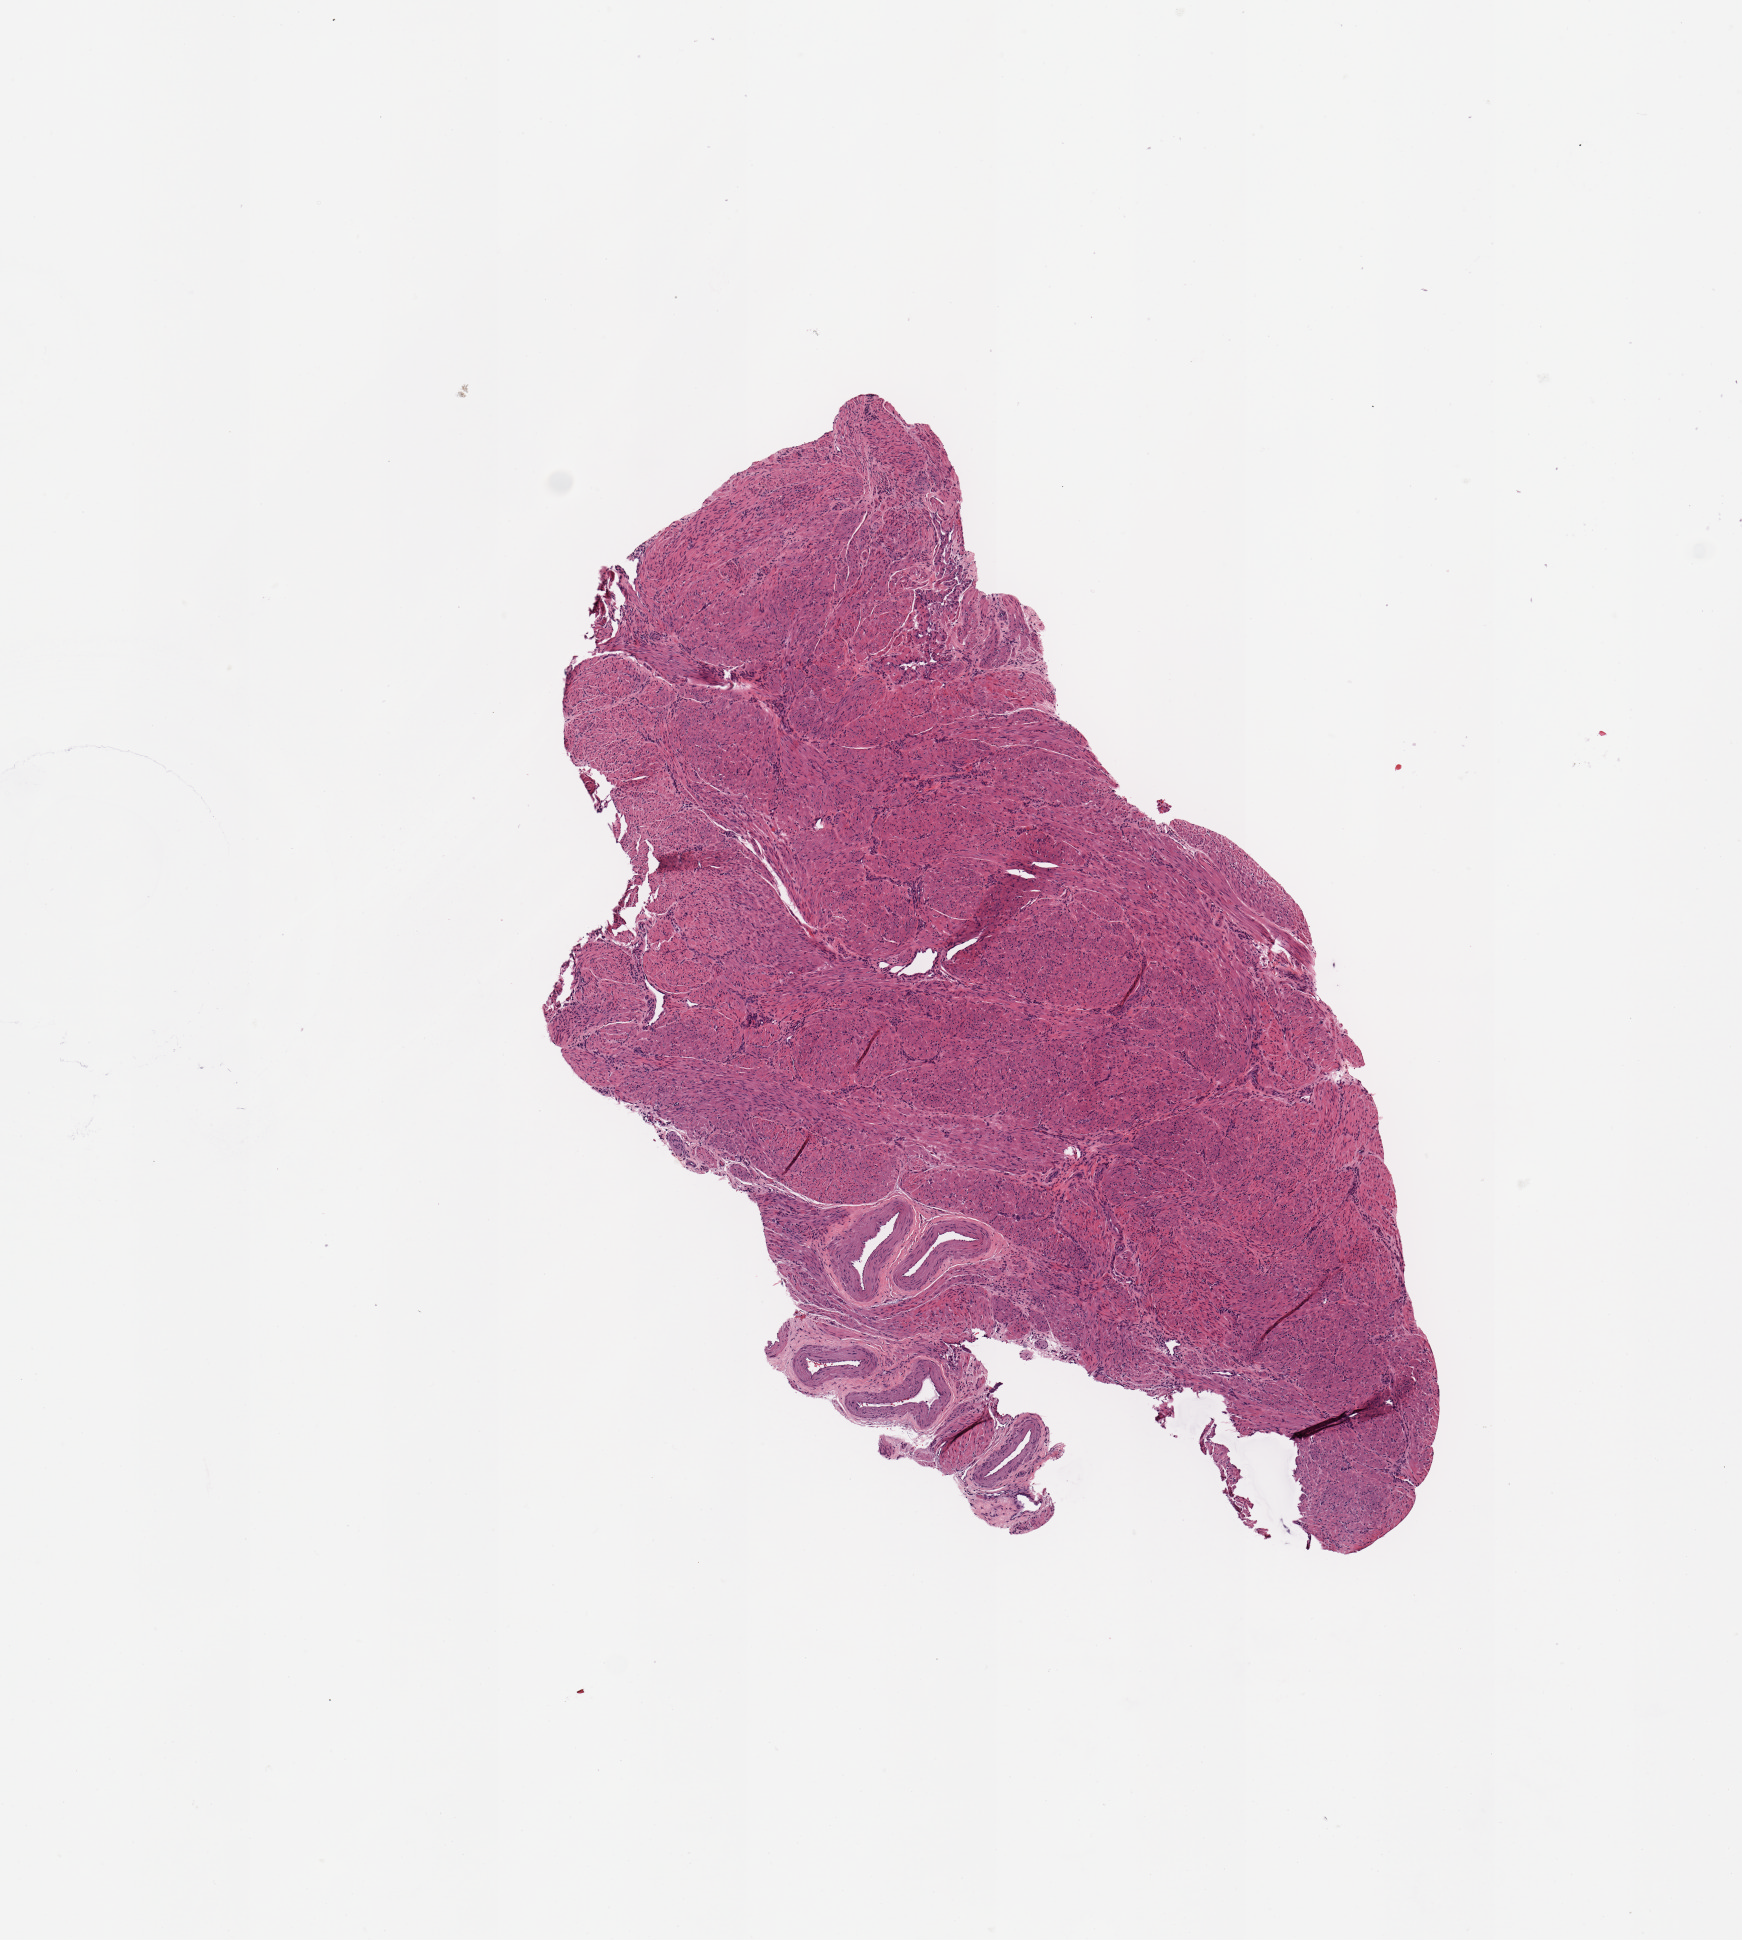
Whole-slide histology image, H&E, shown as a low-resolution overview of the whole scanned area (about 6.9 x 7.7 mm, from a 20x scan), uterus, normal (non-tumour) tissue. 54-year-old female patient.
* this section: normal (non-tumour) tissue from the same patient
* patient diagnosis: Endometrioid adenocarcinoma, NOS